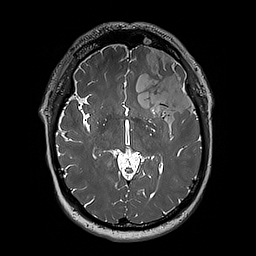
Brain MRI from a brain-tumour surgery series, one axial slice. Position 117 of 192 along the scan axis. 1 mm slice thickness. 256 × 256 image matrix. Case-level facts recorded for this patient, not image findings: histopathology: Oligodendroglioma; WHO grade: 3; IDH mutation: yes; tumour location: Left Sylvian Fissure (Temporal).
Structures marked on this image (expert manual segmentation):
- tumour: bounding box <124,49,197,122> (left, top, right, bottom; pixels)